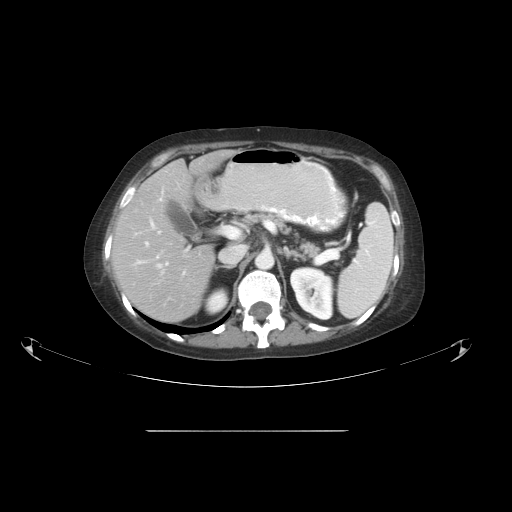
Contrast-enhanced abdominal CT, one axial slice; position 32 of 51 along the scan axis; reconstruction kernel STANDARD; intravenous contrast given; soft-tissue window (W 400 / L 40 HU); 512 × 512 image matrix, field of view 475 × 475 mm. Female patient, age 48 years. Case-level facts recorded for this patient, not image findings: diagnosis: colorectal cancer liver metastases, imaged before liver resection; multiple liver metastases: yes; largest metastasis: 1 cm; chemotherapy before resection: no.
Structures marked on this image (outlined manually by an expert reader):
- hepatic veins: bounding box [x1, y1, x2, y2] px = [146, 198, 169, 273]
- liver: [112, 153, 228, 323]
- planned liver remnant (the part of the liver to remain after resection): [112, 160, 215, 323]
- portal vein (with intrahepatic branches): [134, 220, 189, 274]